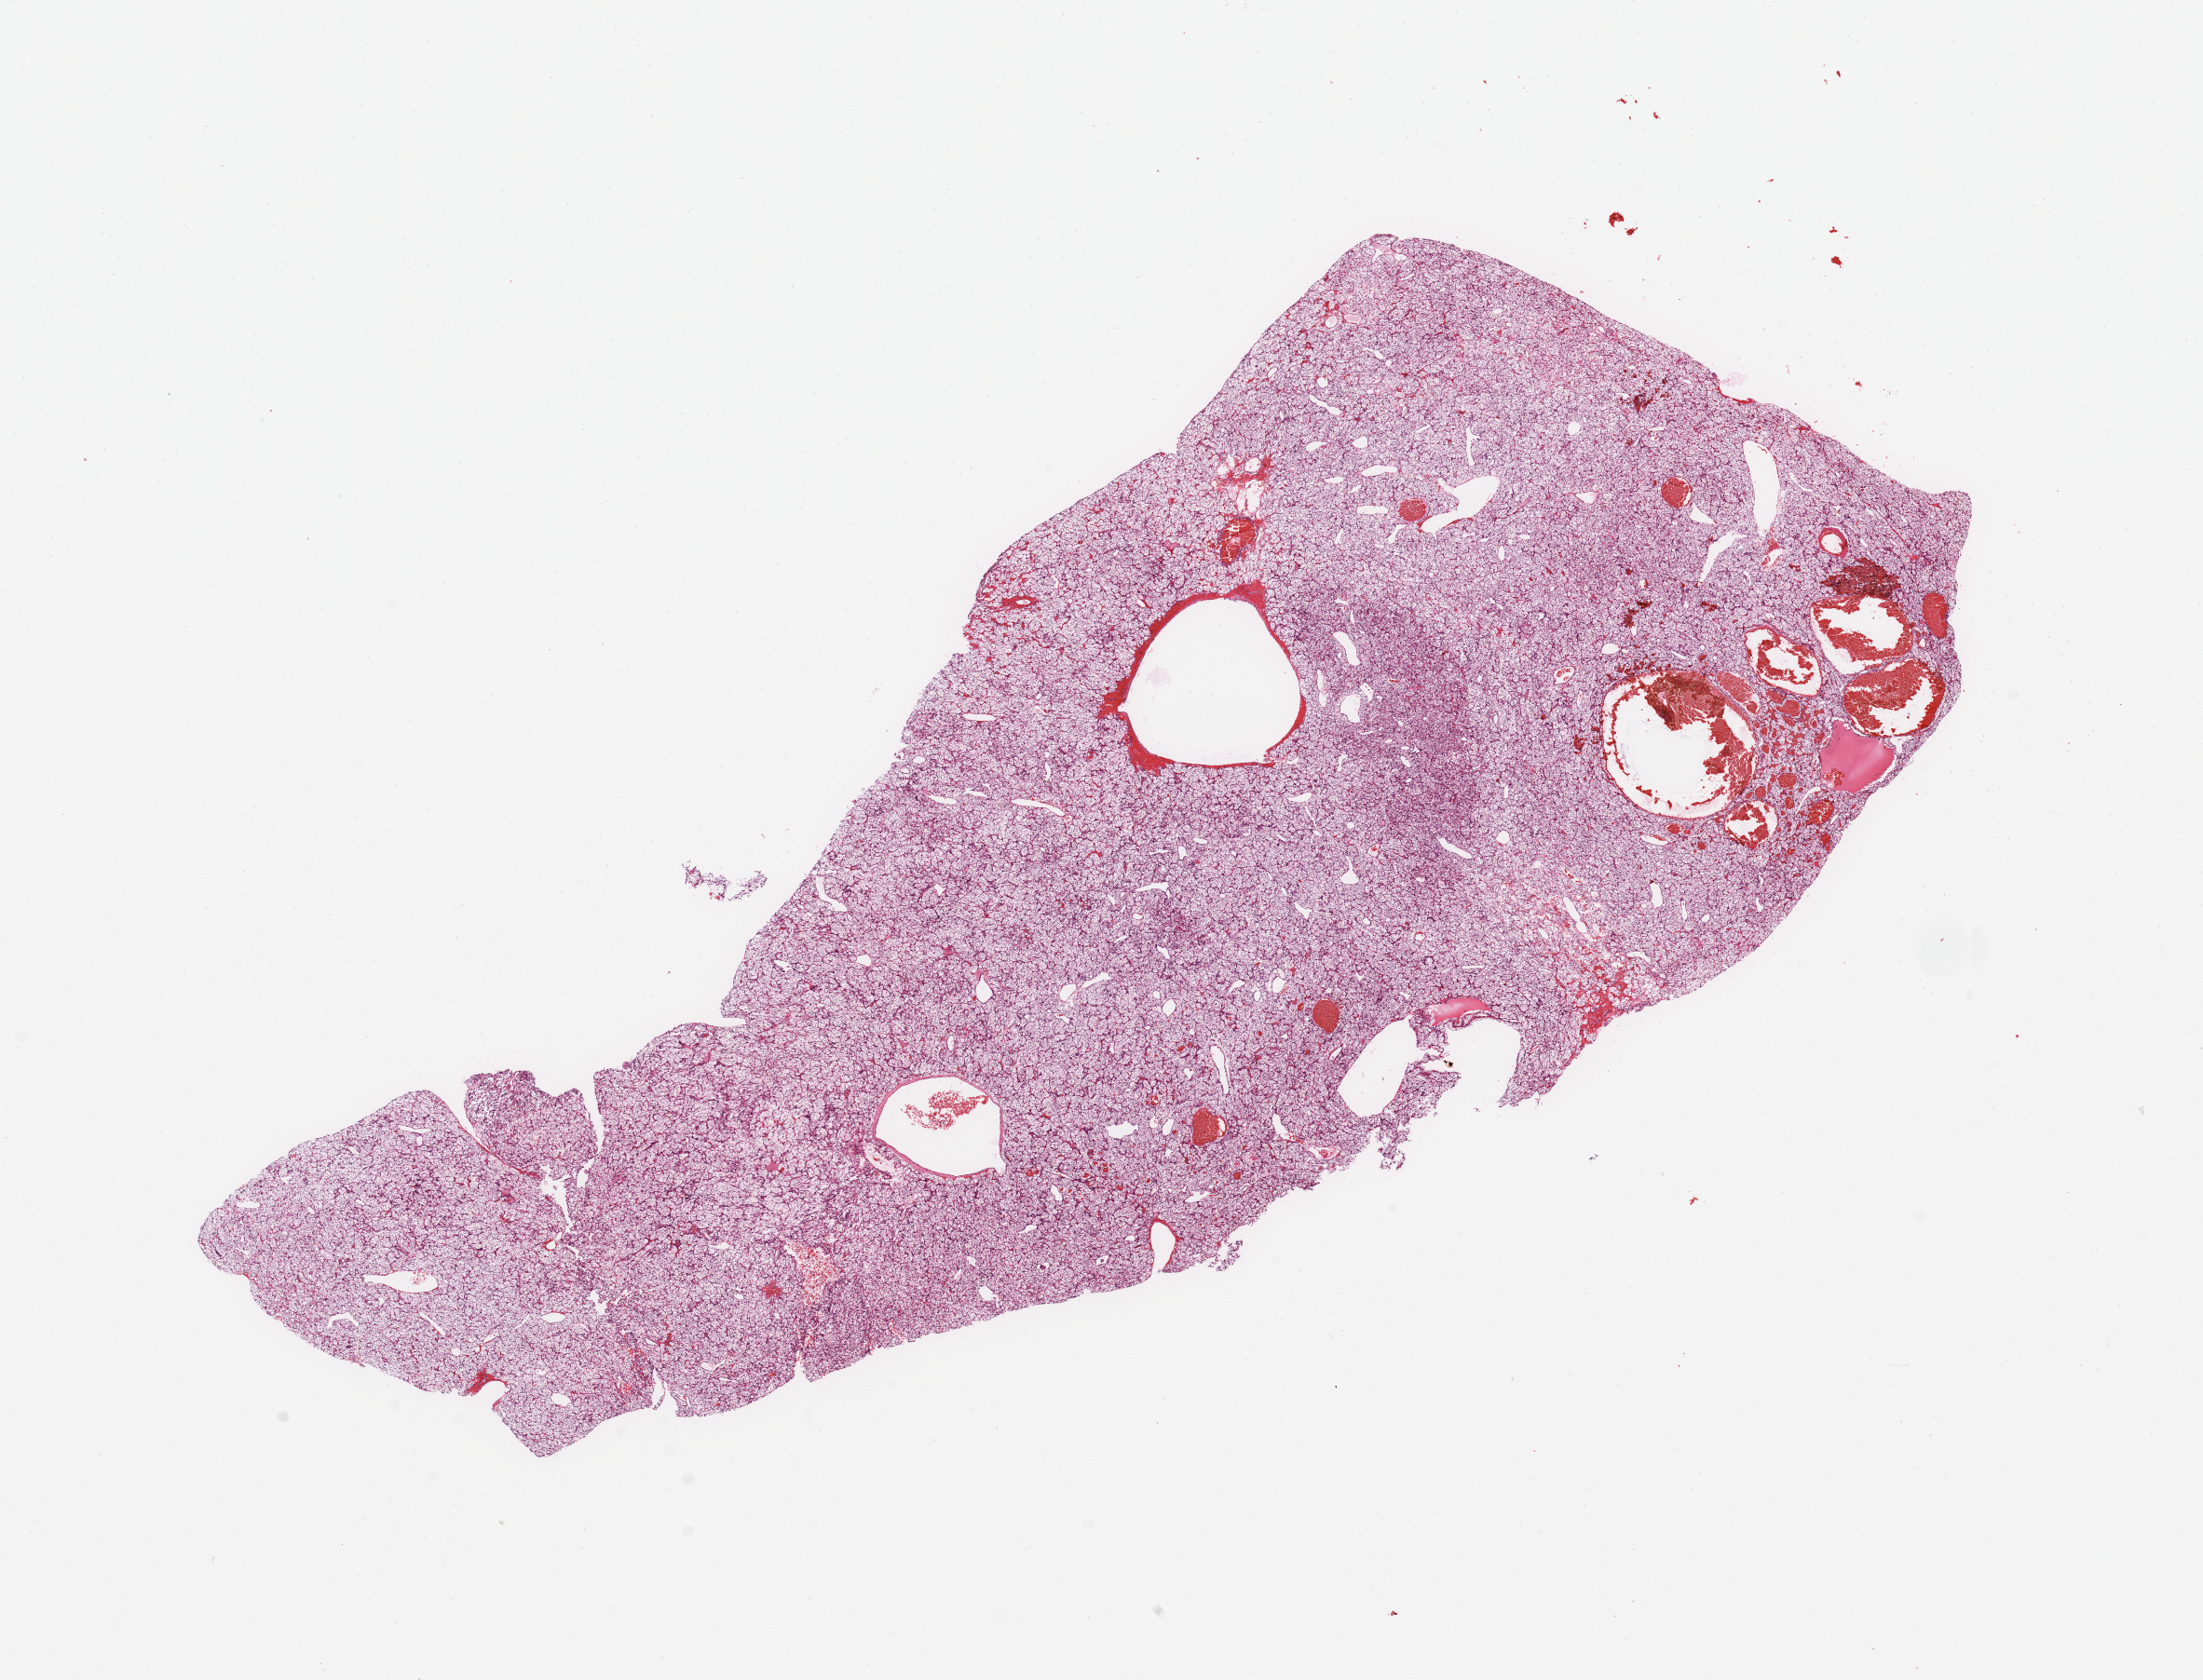
Whole-slide histology image, H&E — a low-resolution overview of the entire scanned area, about 18.7 x 14.3 mm (from a 20x scan); tumour tissue sample, sampled site: kidney. 56-year-old female patient. Histologic grade: G2 (moderately differentiated). Slide review estimates, as recorded: tumour nuclei 95%, necrosis 0%.
AJCC pathologic stage: III. Histologic diagnosis: Renal cell carcinoma, NOS.